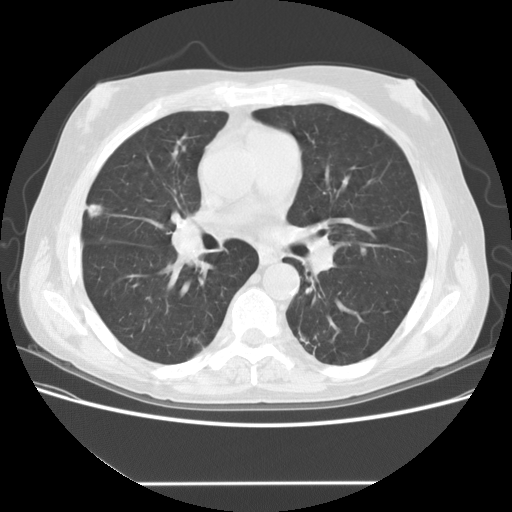
Low-dose screening chest CT, one axial slice. Slice 88 of 153 in the series (ordered by position). 120 kVp. Lung window (W 1500 / L -600 HU). 2.5 mm slice thickness. 512 × 512 image matrix, field of view 360 × 360 mm.
Annotated regions visible in this slice (manually delineated by an expert):
- lesion 2 (tumor, upper lobe of right lung): bounding box (x1, y1, x2, y2) in pixels: (88, 204, 102, 217)